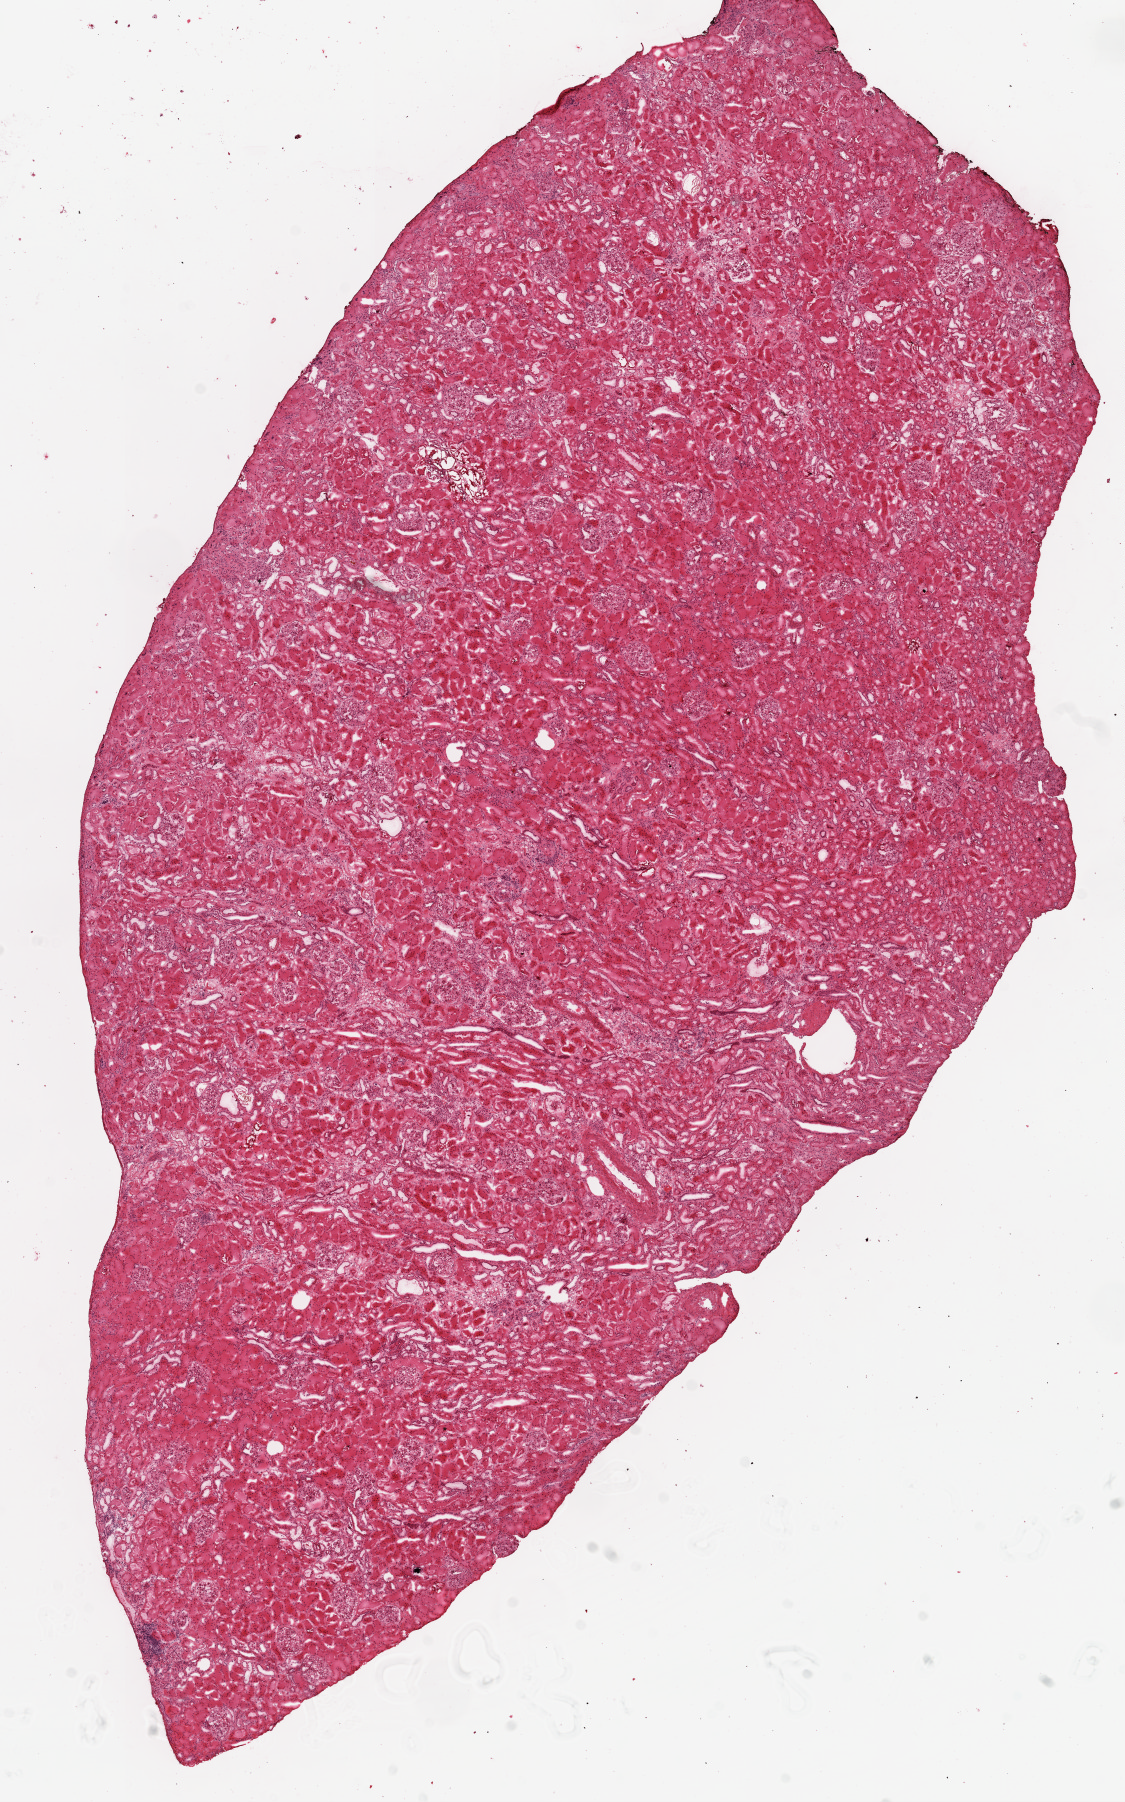
Hematoxylin and eosin (H&E) stained whole-slide image, a low-resolution overview of the entire scanned area, about 9.0 x 14.5 mm. Frozen section. Kidney, solid tissue normal (non-tumour tissue) sample. Male patient; age at initial diagnosis 60 years.
This section: solid tissue normal (non-tumour) sample from the same patient. Patient diagnosis: Clear cell adenocarcinoma, NOS.